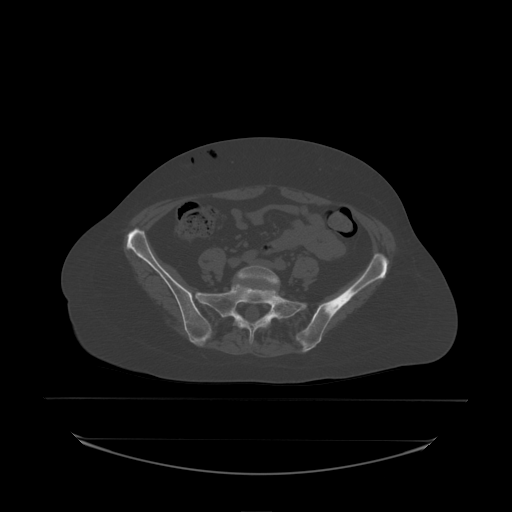
CT including the spine, one axial slice. Position 32 of 242 along the scan axis. Bone window (W 1800 / L 400 HU). 2.5 mm slice thickness. 512 × 512 image matrix, field of view 500 × 500 mm. Female patient, age 53 years. From the clinical record (not read from this slice): primary cancer: lung; vertebrae with lytic lesions (as recorded): T7, L1.
Structures marked on this image (semi-automatically segmented with operator editing):
- L5 vertebra: box from (x=237, y=266) to (x=280, y=291) px